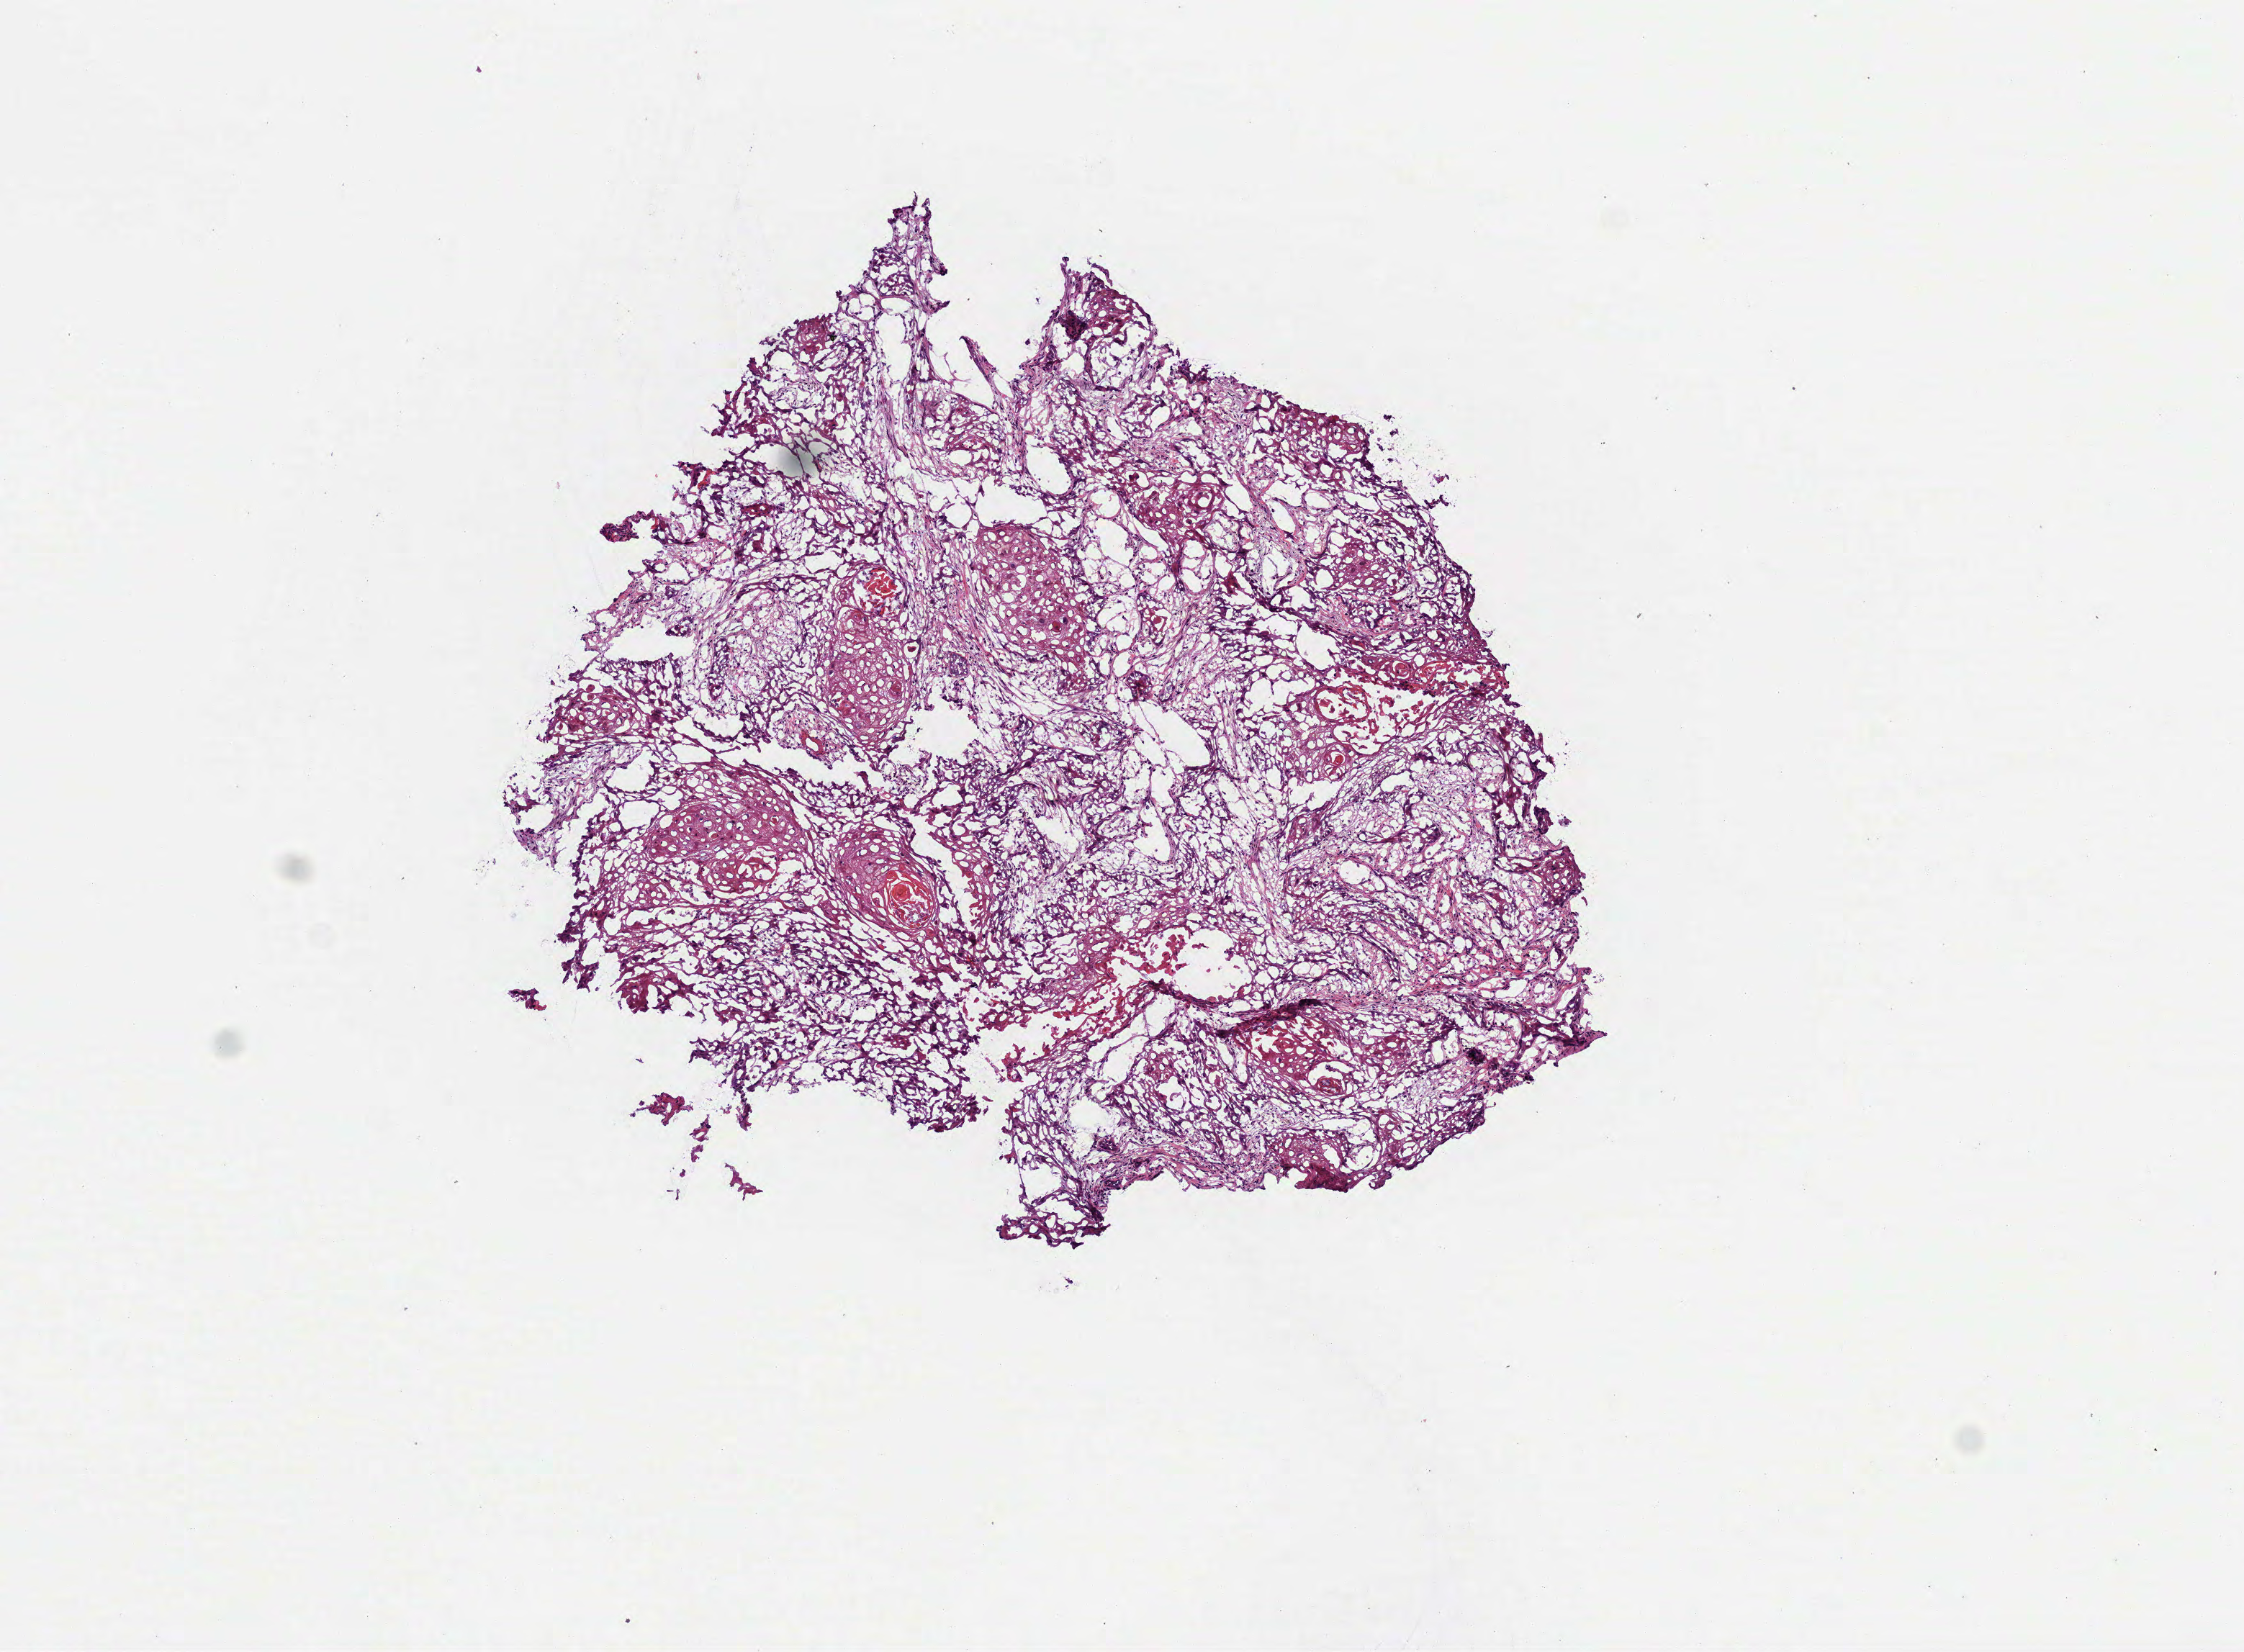
Digitized Hematoxylin and eosin (H&E) stained tissue section (whole slide) — shown as a low-resolution overview of the whole scanned area (about 6.3 x 4.6 mm), frozen section from the bottom of the tissue portion, sample: primary tumour, head and neck. Male patient; age at initial diagnosis 41 years. Histologic grade: G2 (moderately differentiated). Slide review estimates, as recorded: tumour cells 99%, tumour nuclei 90%, normal cells 0%, stromal cells 0%, necrosis 1%. Inflammatory infiltration, as recorded: lymphocyte infiltration 5%, monocyte infiltration 0%, neutrophil infiltration 1%.
AJCC pathologic stage: IVA (7th edition). Pathologic diagnosis: Squamous cell carcinoma, NOS (tongue, NOS).